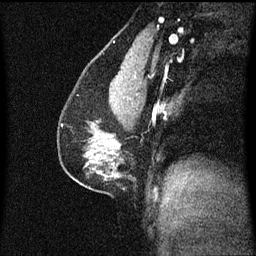
Breast MRI (dynamic contrast-enhanced), one sagittal slice; position 33 of 60 along the scan axis; dynamic contrast-enhanced series, image 2 of 3 at this slice position (ordered by acquisition); 1.5 T; TE 4.2 ms, TR 8.4 ms; 256 × 256 image matrix, field of view 200 × 200 mm. Female patient, age 41 years. From the clinical record (not read from this slice): setting: breast cancer imaged before/during neoadjuvant chemotherapy; receptor status: triple-negative.
Annotated regions visible in this slice (semi-automatically segmented with operator editing):
- analysis volume of interest (the breast-tissue region the enhancement analysis was run in; not a lesion): box from (x=58, y=104) to (x=125, y=175) px
- tumour enhancement mask (voxels above the 70 % enhancement threshold inside the analysis volume of interest): (x=108, y=140)–(x=120, y=147)